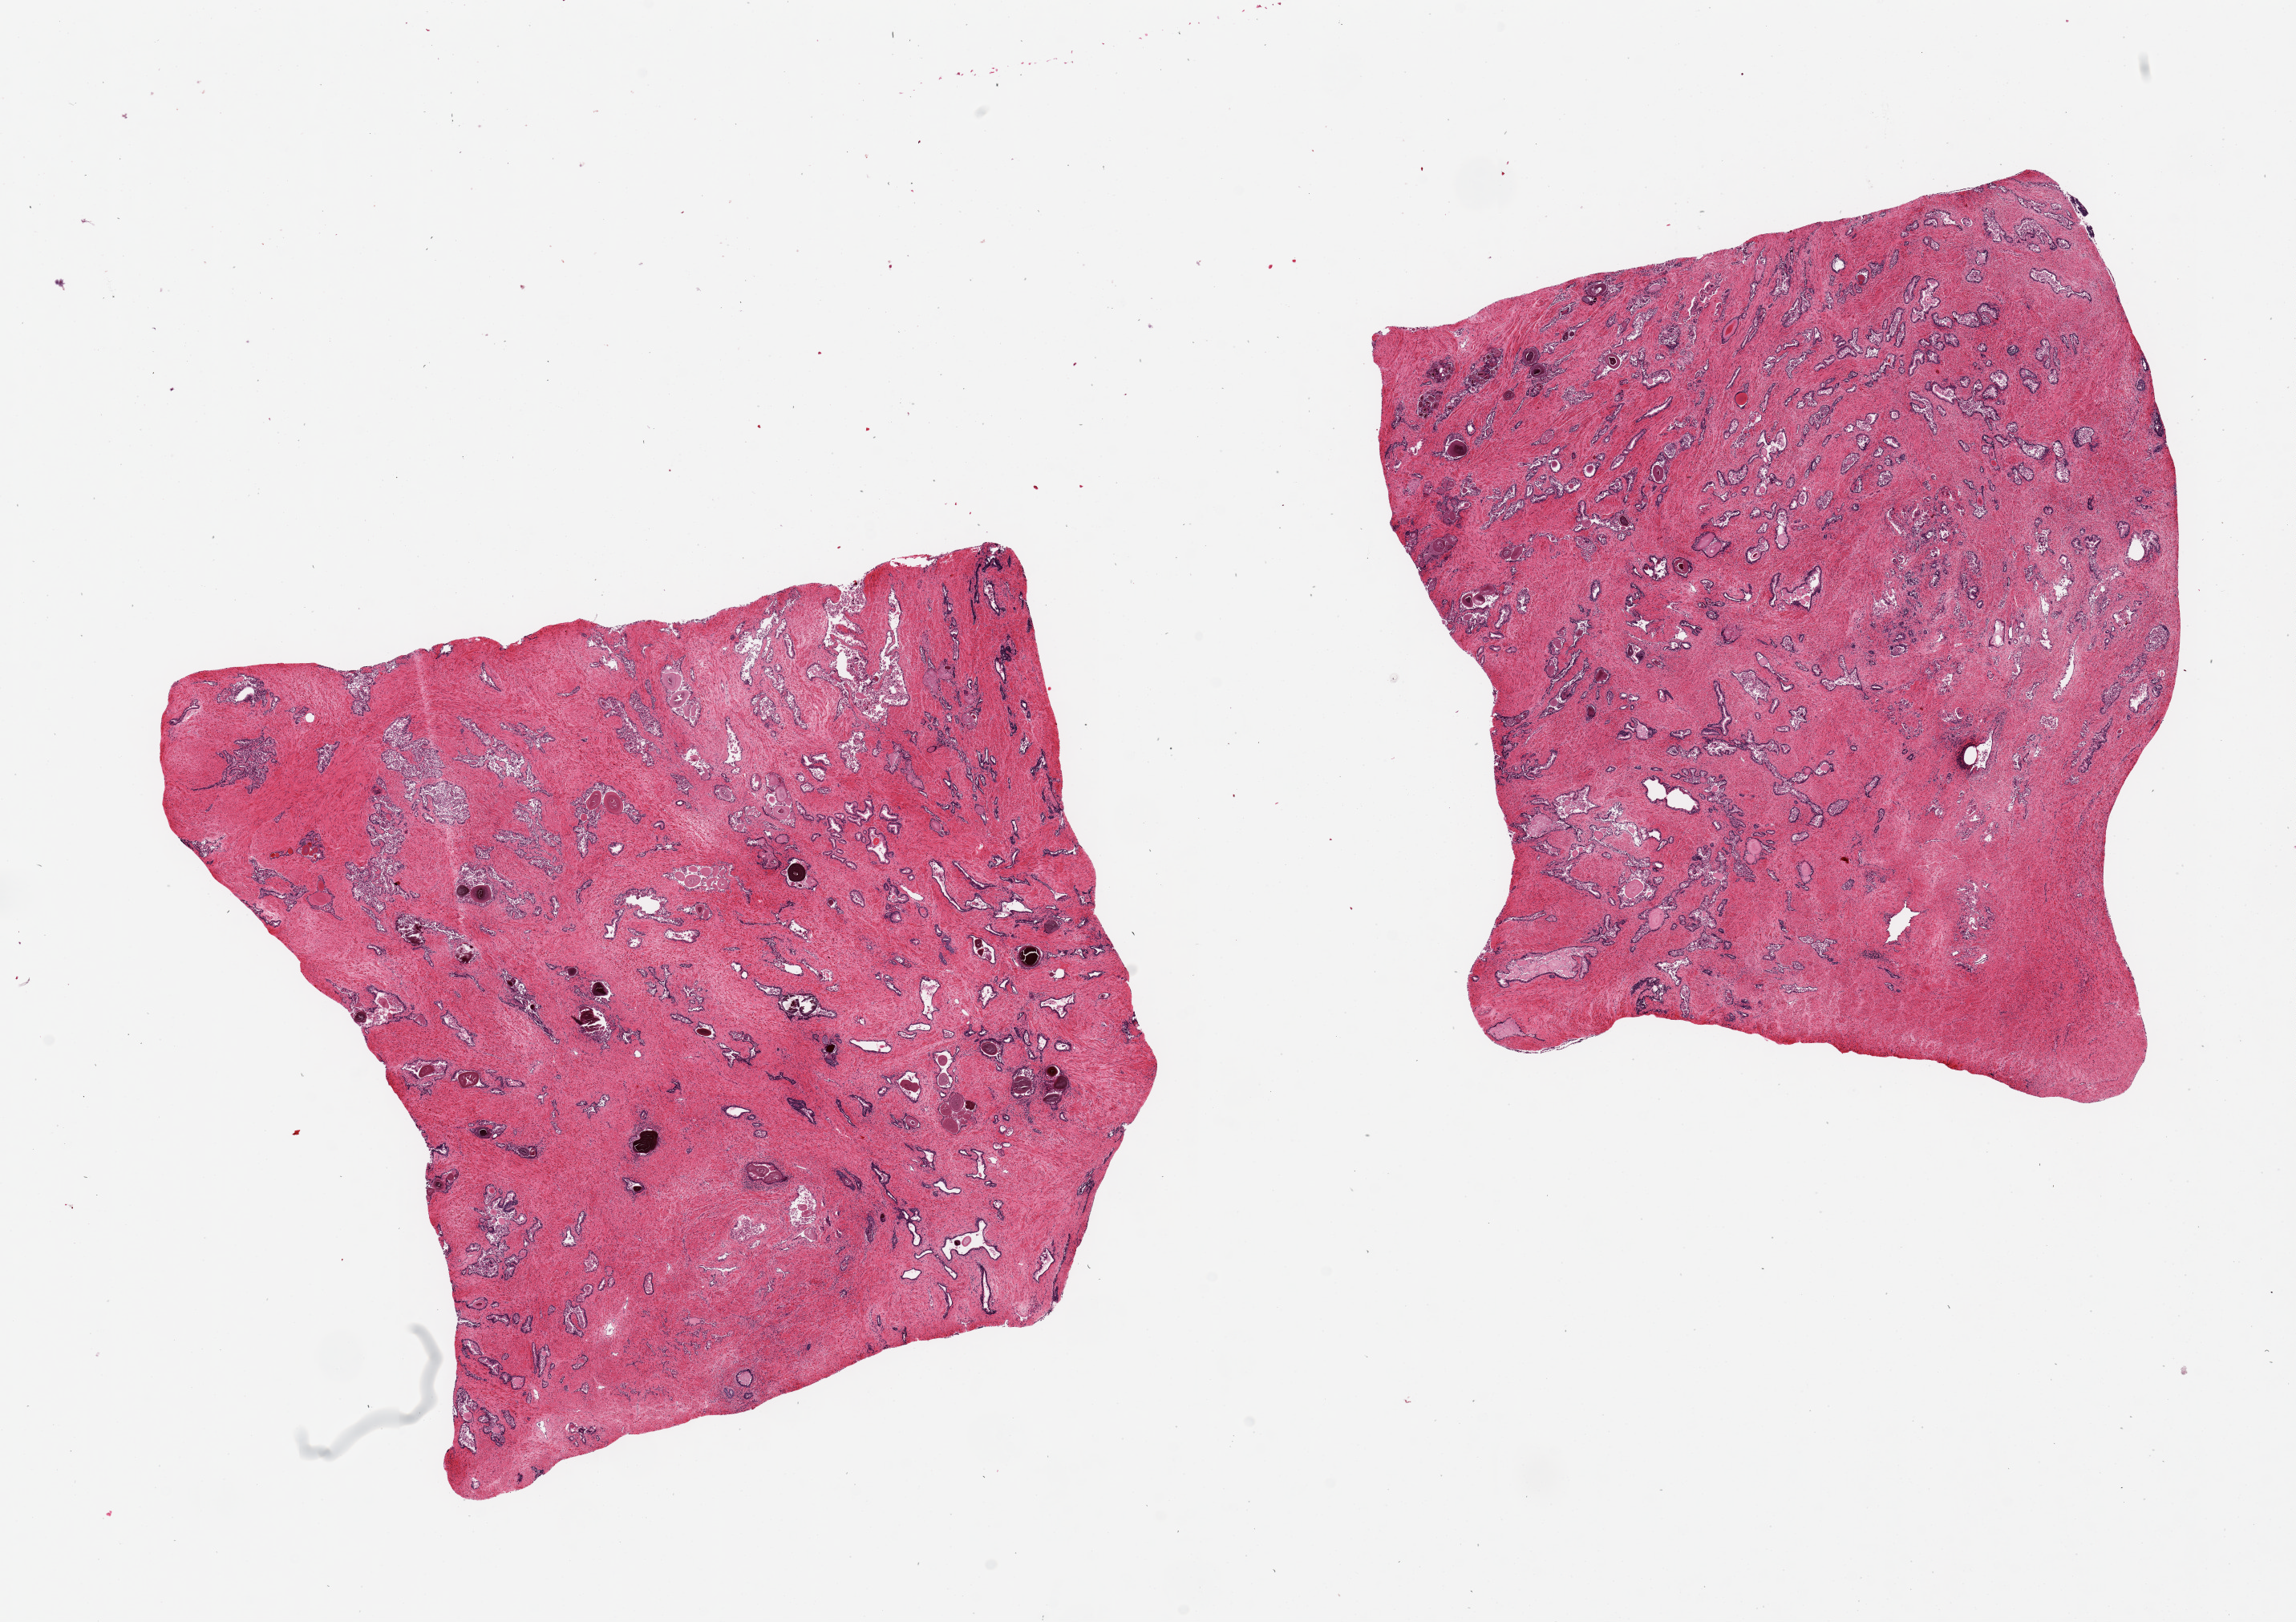
Whole-slide image, hematoxylin and eosin (H&E) stain, low-resolution overview of the scanned area, about 22.6 x 16.0 mm (from a 20x scan). PAXgene-fixed, paraffin-embedded tissue. Target tissue: prostate. Donor tissue sample.
* reviewer comment on this tissue sample: 2 pieces, 9x8.5 & 9x7mm